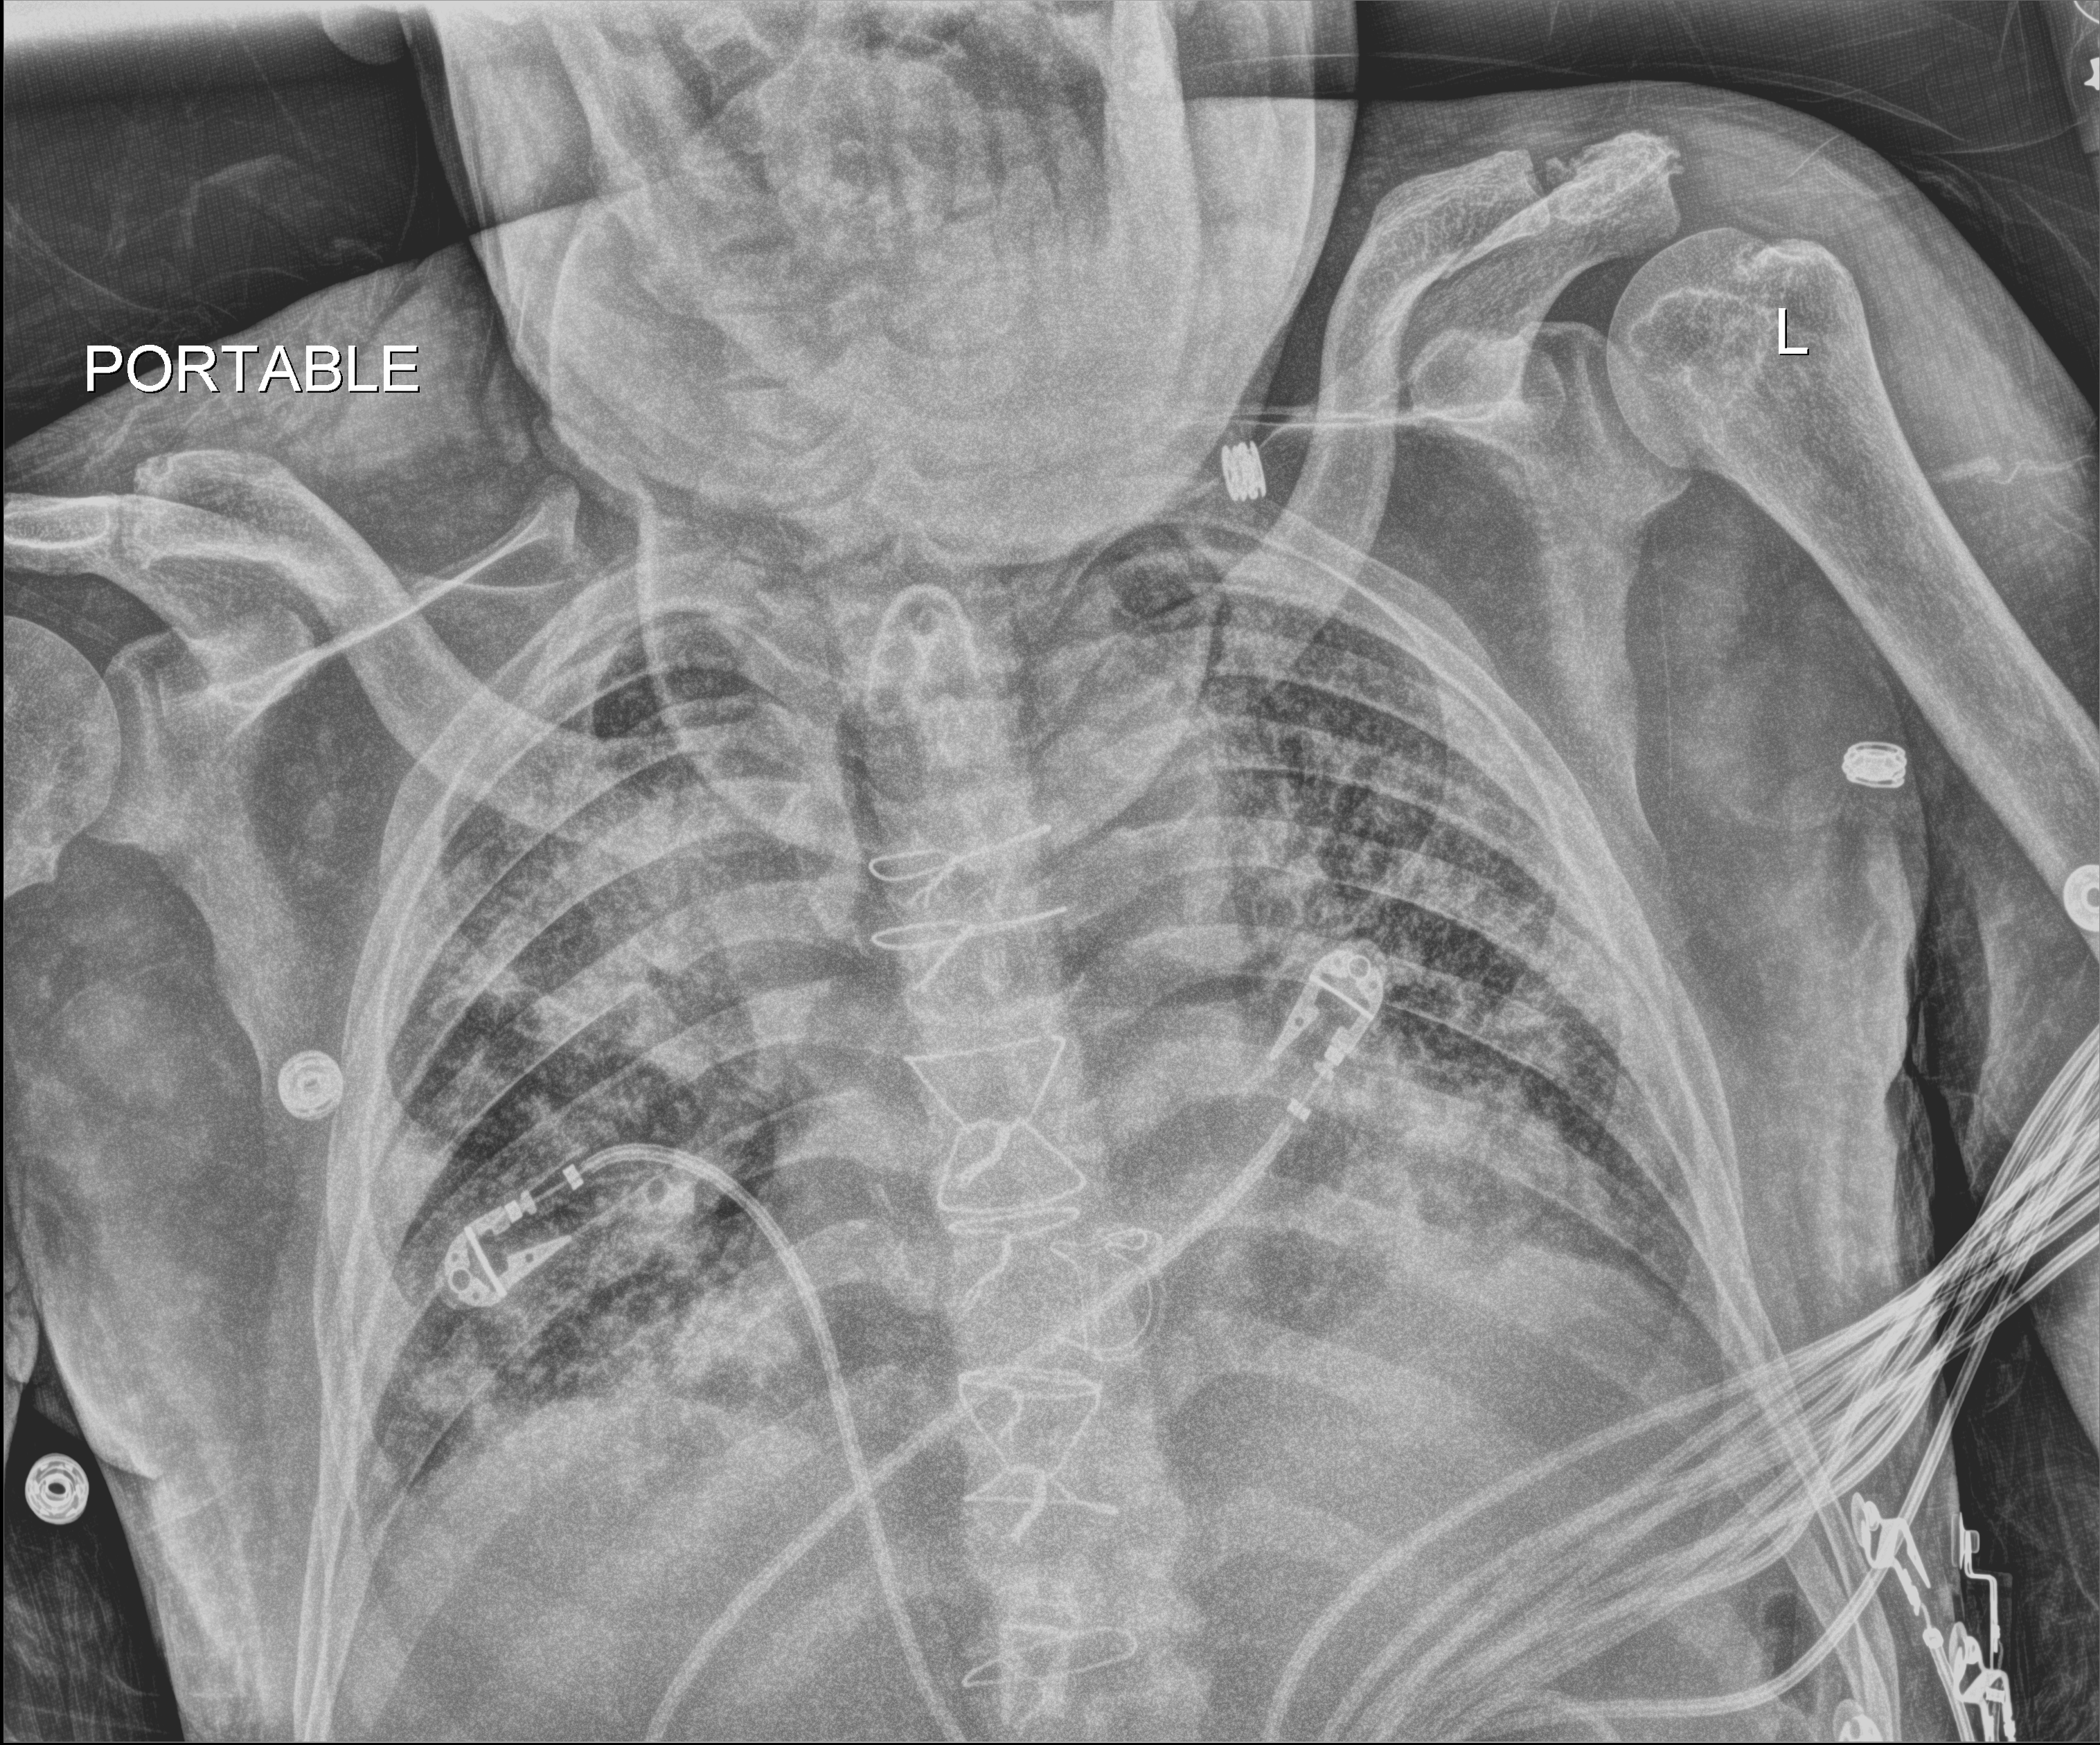
Bedside chest radiograph (digital radiography); anteroposterior (AP) projection. Patient hospitalised with COVID-19; male, aged 60–74 years.
Admission-level facts for this patient (not findings on this image; timing relative to this image not recorded): admitted to intensive care during this hospital stay: yes.